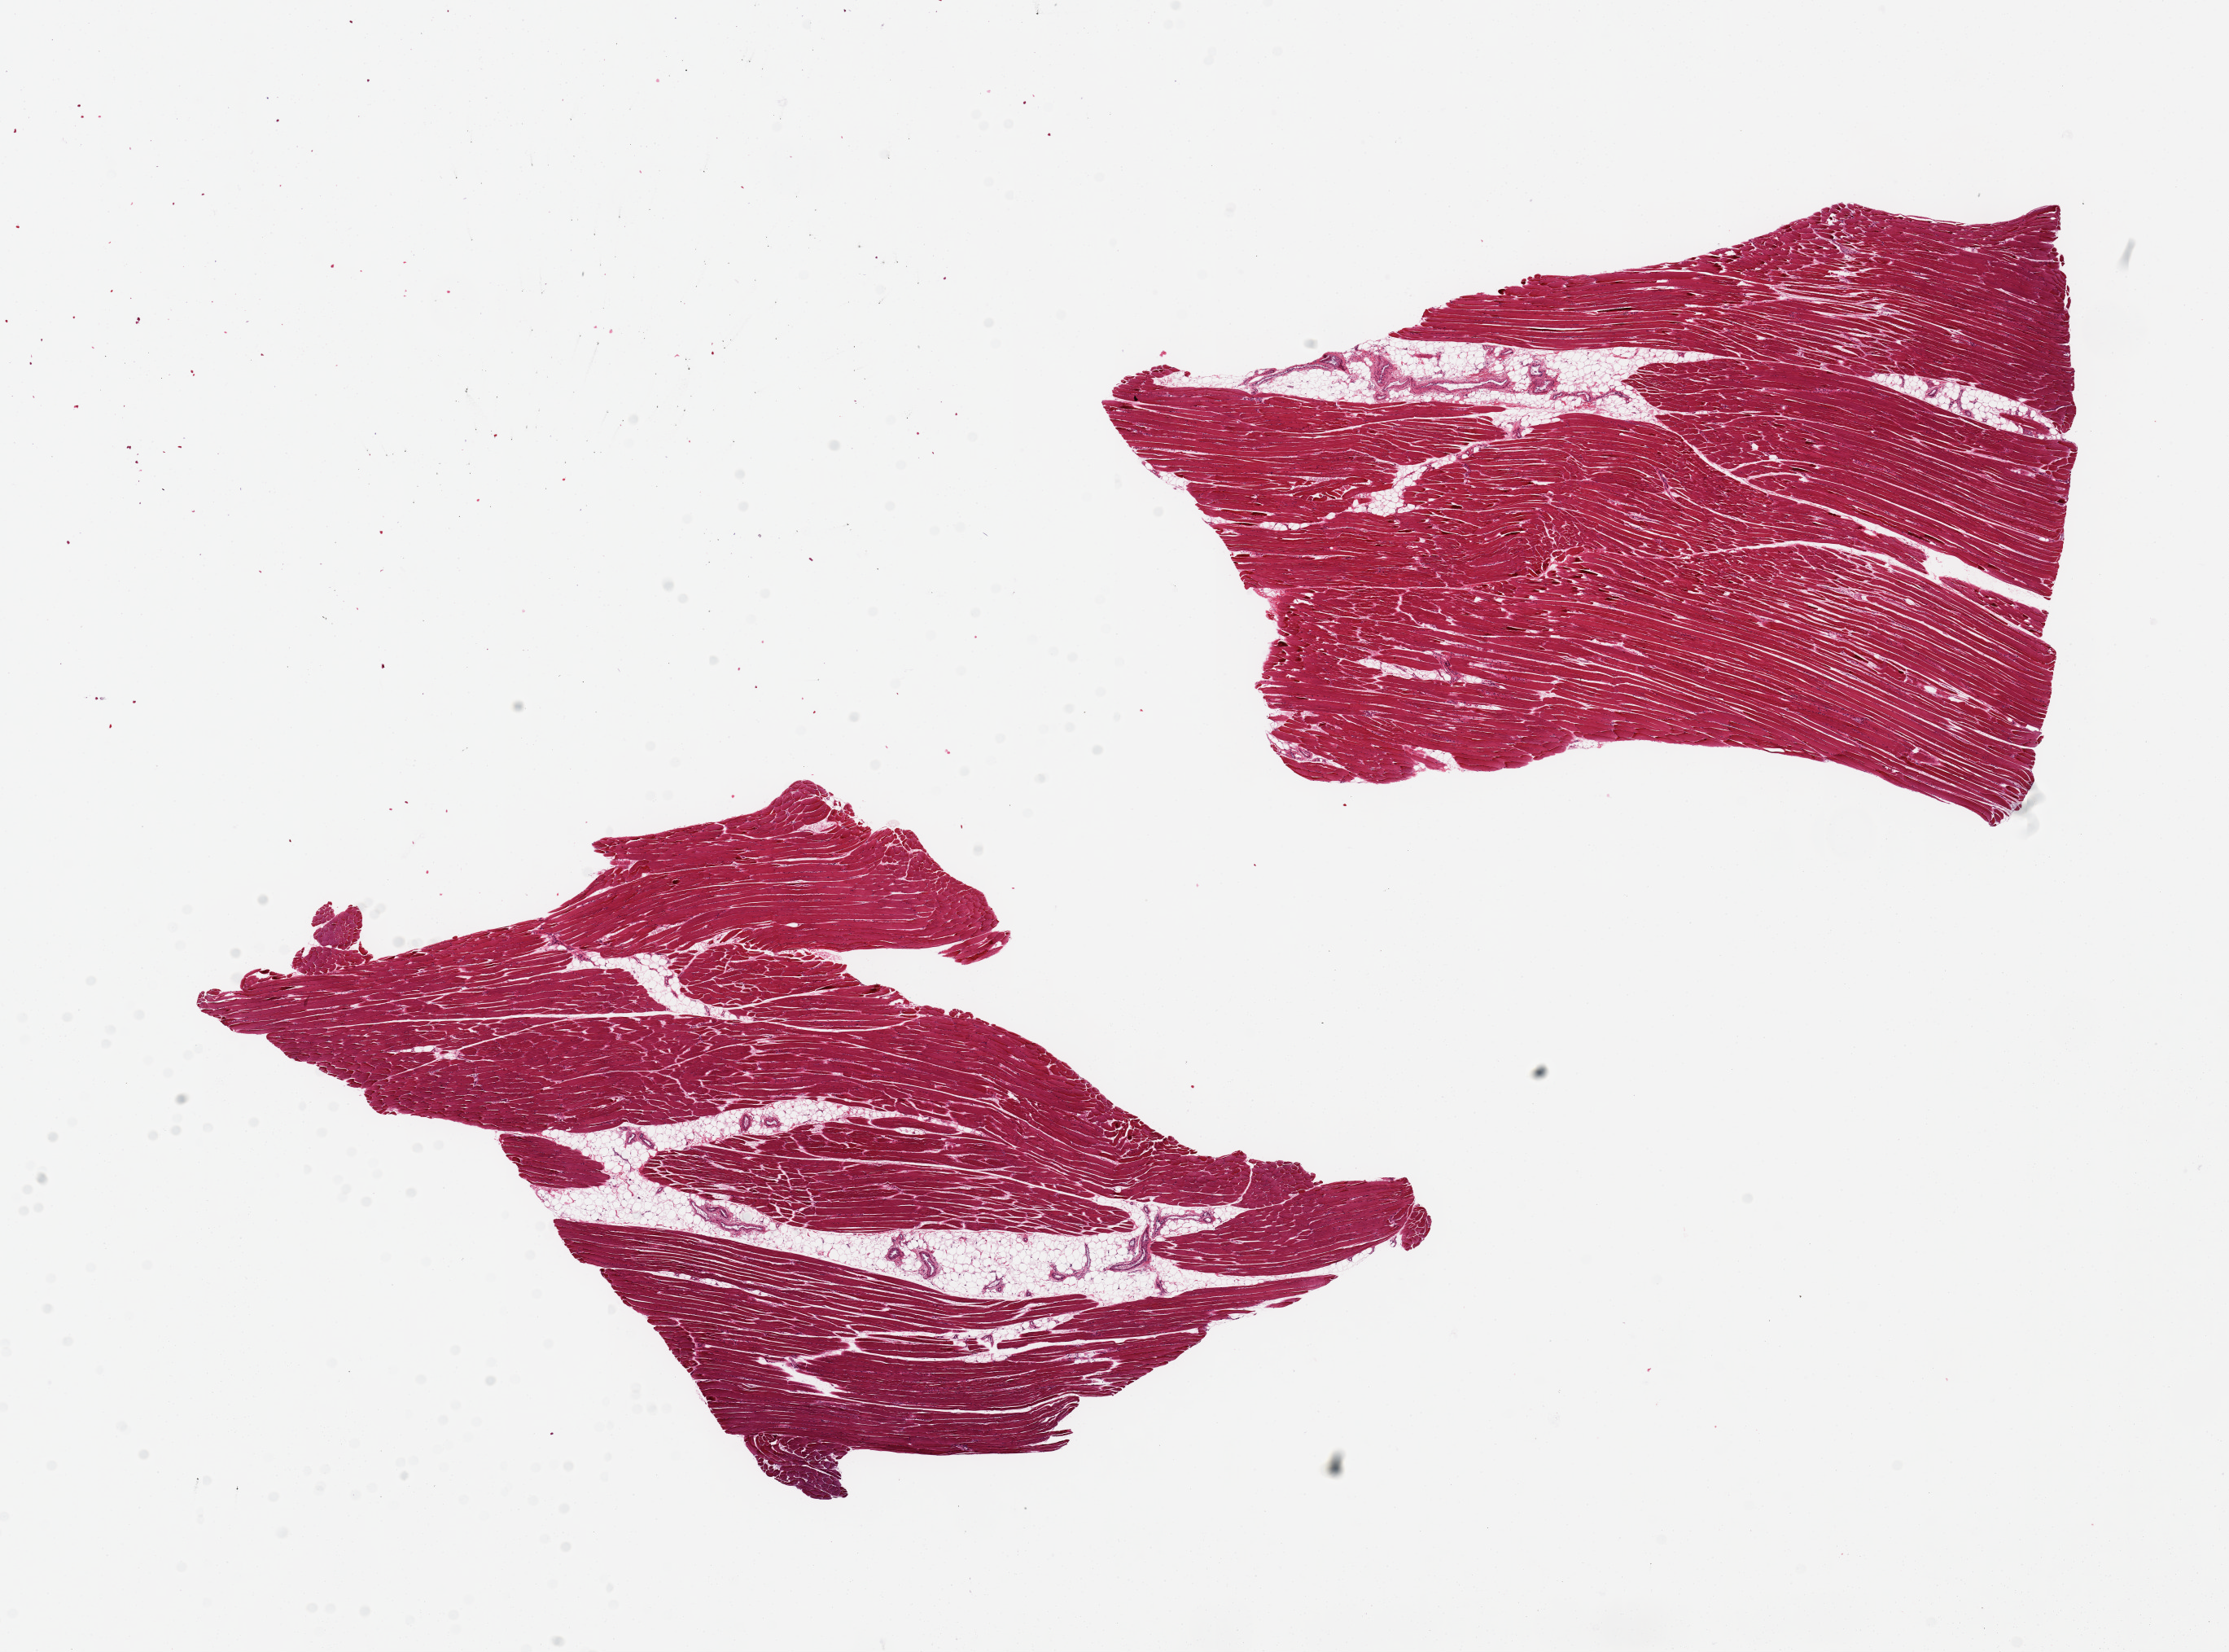
Haematoxylin and eosin whole-slide image — low-resolution overview of the scanned area, about 21.7 x 16.0 mm (acquisition: 20x scan). PAXgene-fixed, paraffin-embedded tissue. Target tissue: skeletal muscle. Donor tissue sample. Donor: female.
Review note (as recorded): 2 pieces, 8x7 & 9x6mm; 10% internal adipose.